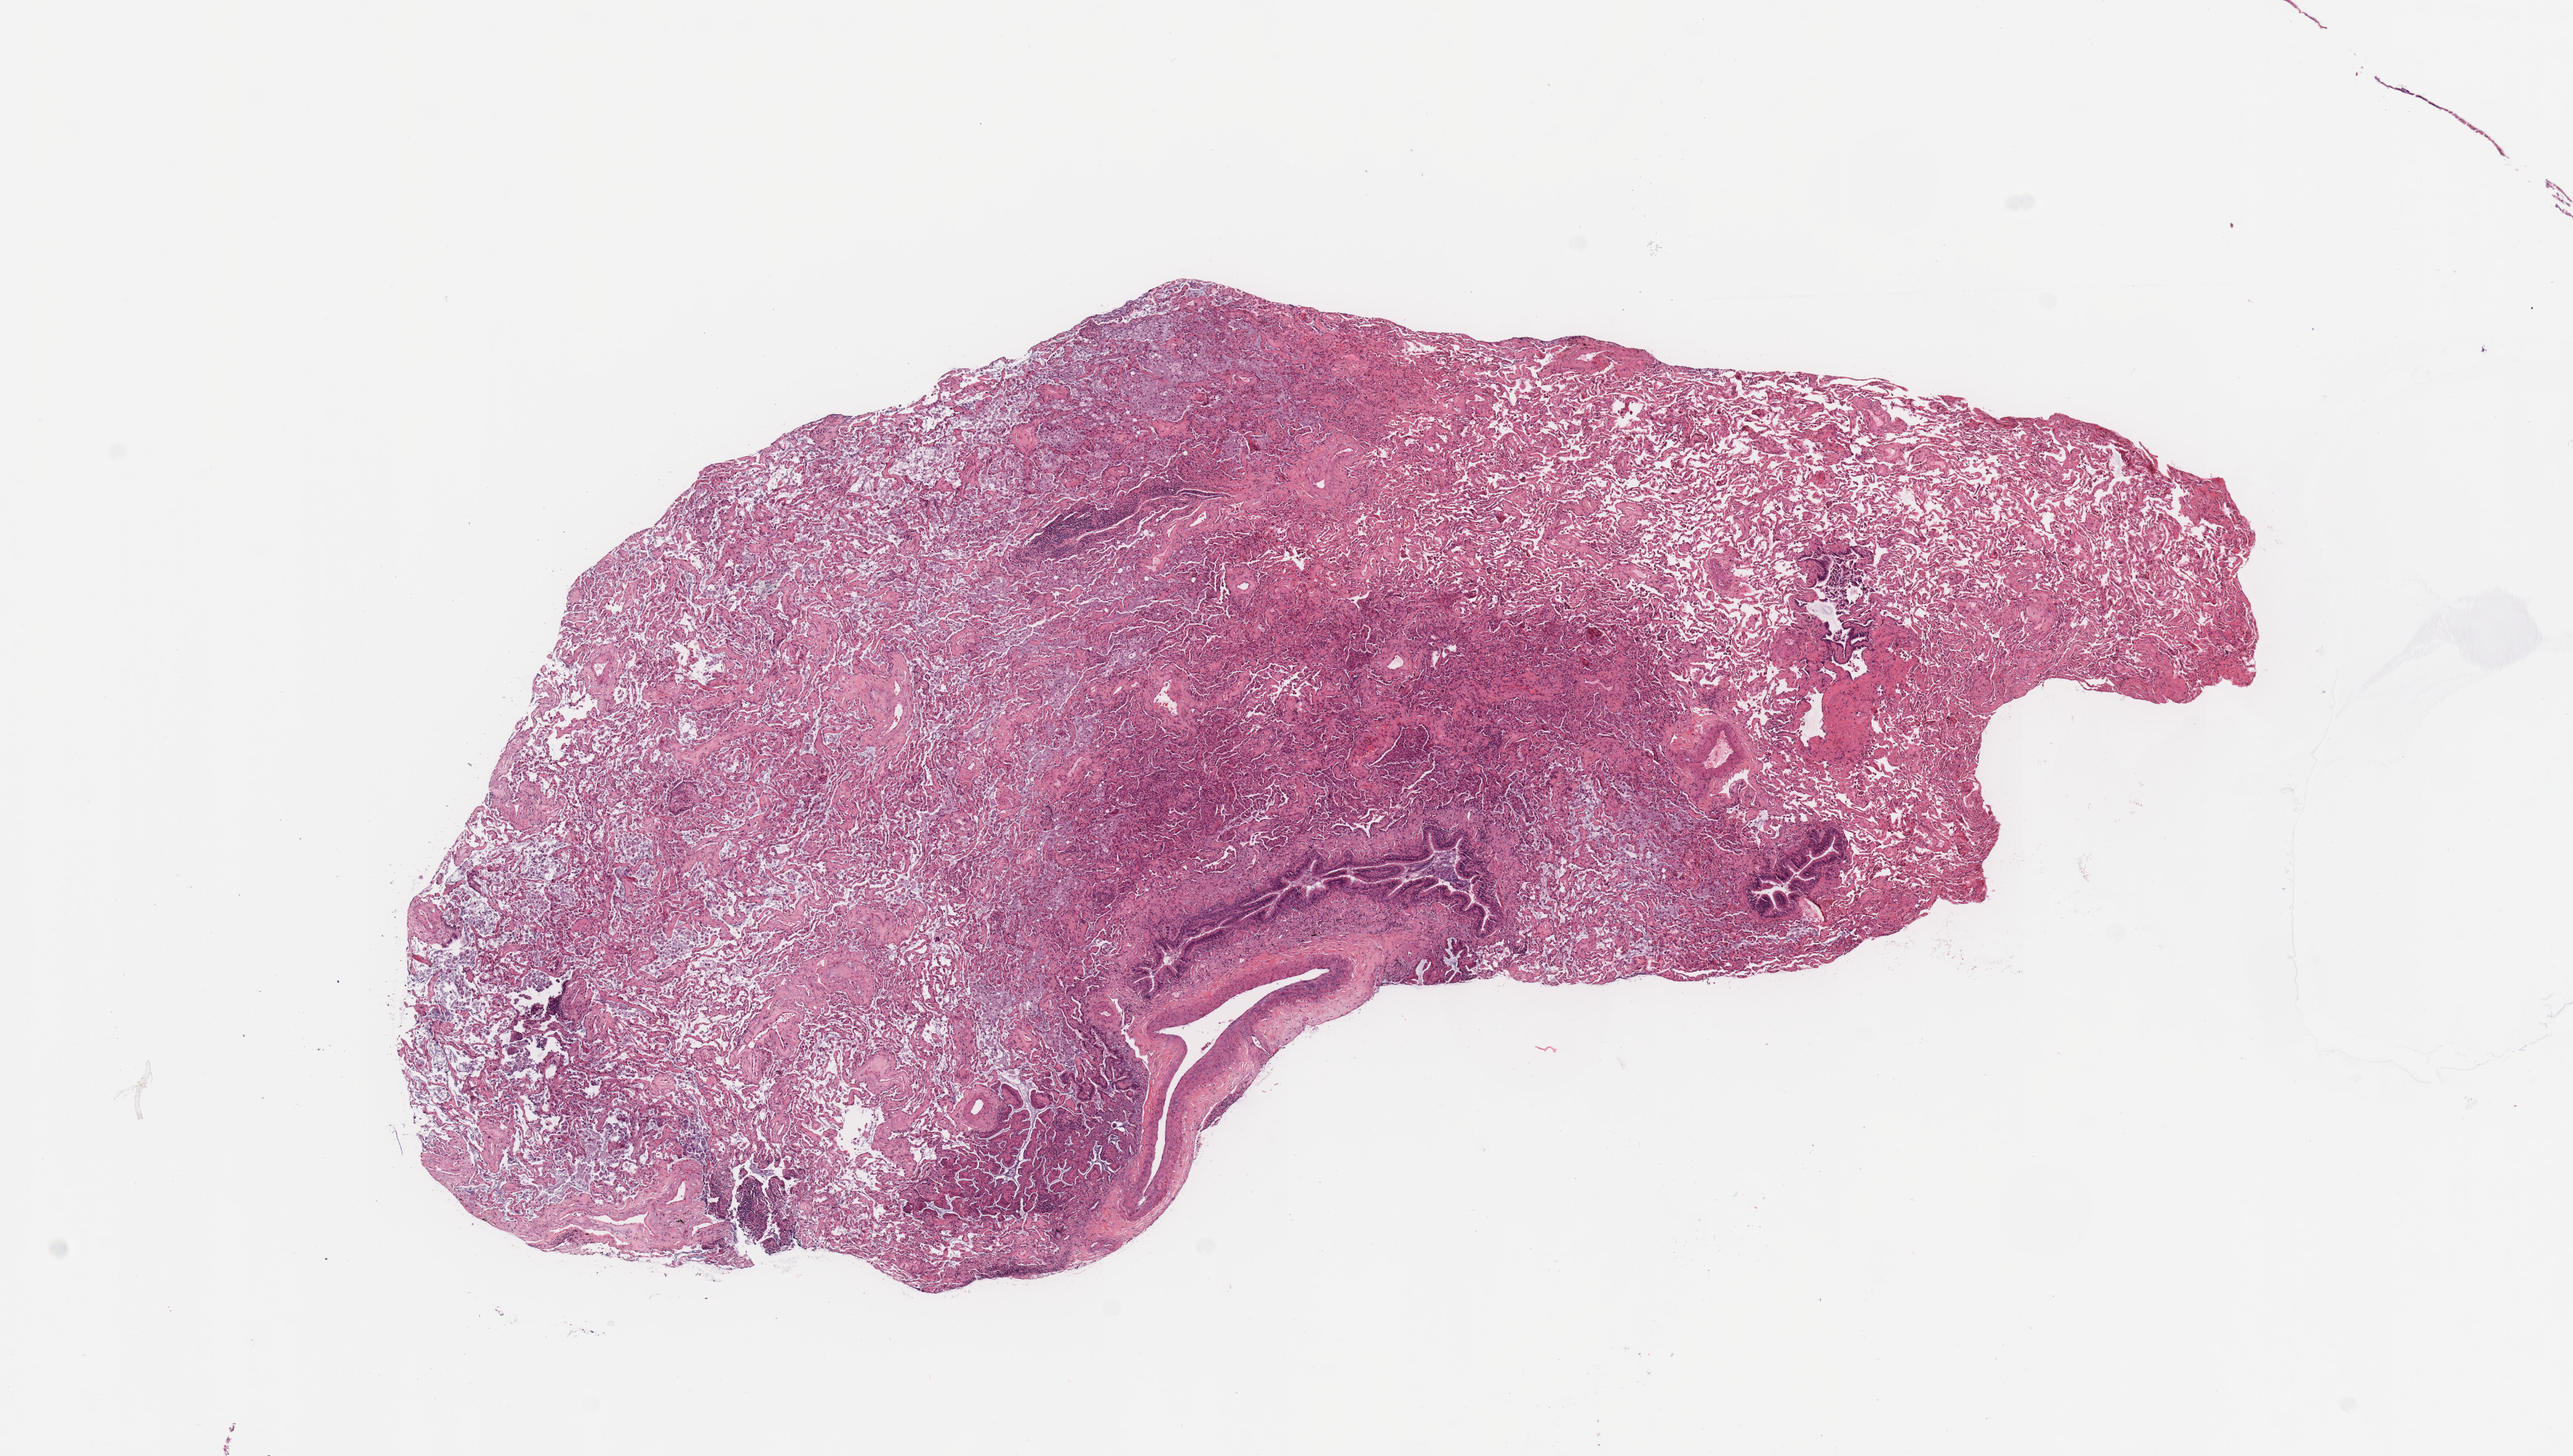
Digitized Hematoxylin and eosin (H&E) stained tissue section (whole slide), whole scanned area (about 13.8 x 7.8 mm, acquisition: 20x scan) shown as a low-resolution overview, tumour tissue sample, lung. Female, 78 y/o.
Histologic diagnosis: Adenocarcinoma, NOS.